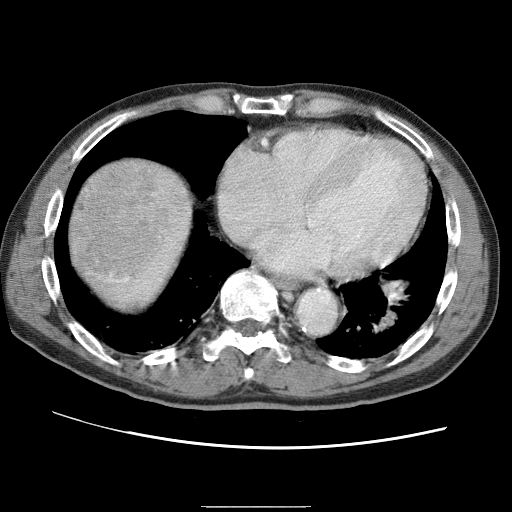
Contrast-enhanced abdominal CT (liver protocol), one axial slice. Position 66 of 75 along the scan axis. Reconstruction kernel STANDARD. One of 2 acquisitions stored at this slice position. Soft-tissue window (W 400 / L 40 HU). 512 × 512 image matrix. Case-level facts recorded for this patient, not image findings: diagnosis: hepatocellular carcinoma (patient treated with transarterial chemoembolisation; whether this scan precedes or follows treatment is not stated here); TNM stage (as recorded): Stage-II; Child-Pugh class: A; tumour differentiation: well differentiated; tumour size: 2 cm.
Annotated regions visible in this slice (semi-automatic segmentation, software-assisted and operator-edited):
- liver parenchyma outside the tumour (the mass and vessels are separate outlines, so this box may not span the whole liver): box from (x=66, y=152) to (x=202, y=312) px
- mass: (x=66, y=158)–(x=171, y=291)
- liver vessels: (x=130, y=156)–(x=133, y=158)